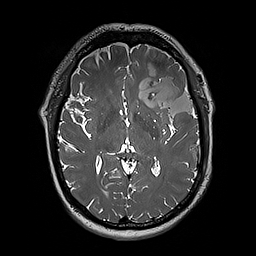
Brain MRI from a brain-tumour surgery series, one axial slice; slice 111 of 192 in the series (ordered by position); 256 × 256 image matrix, field of view 250 × 250 mm. From the clinical record (not read from this slice): histopathology: Oligodendroglioma; WHO grade: 3; IDH mutation: yes.
Structures marked on this image (expert manual segmentation):
- tumour: bounding box <124,64,197,123> (left, top, right, bottom; pixels)